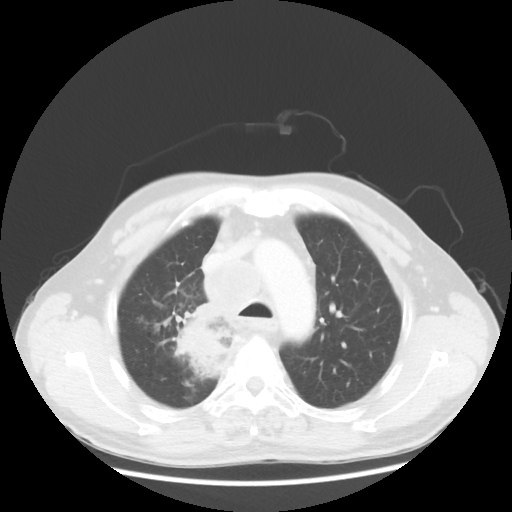
Chest CT, one axial slice. Slice 92 of 124 in the series (ordered by position). Reconstruction kernel STANDARD. 100 kVp. Lung window (W 1500 / L -600 HU). 512 × 512 image matrix. Patient: male, 64 years. From the clinical record (not read from this slice): clinical TNM (as recorded): T3 N3 M0; histopathological grade: G3.
Outlined on this slice (bounding box drawn by a radiologist):
- lung tumour (recorded histology: small cell carcinoma): bounding box <172,303,230,382> (left, top, right, bottom; pixels)